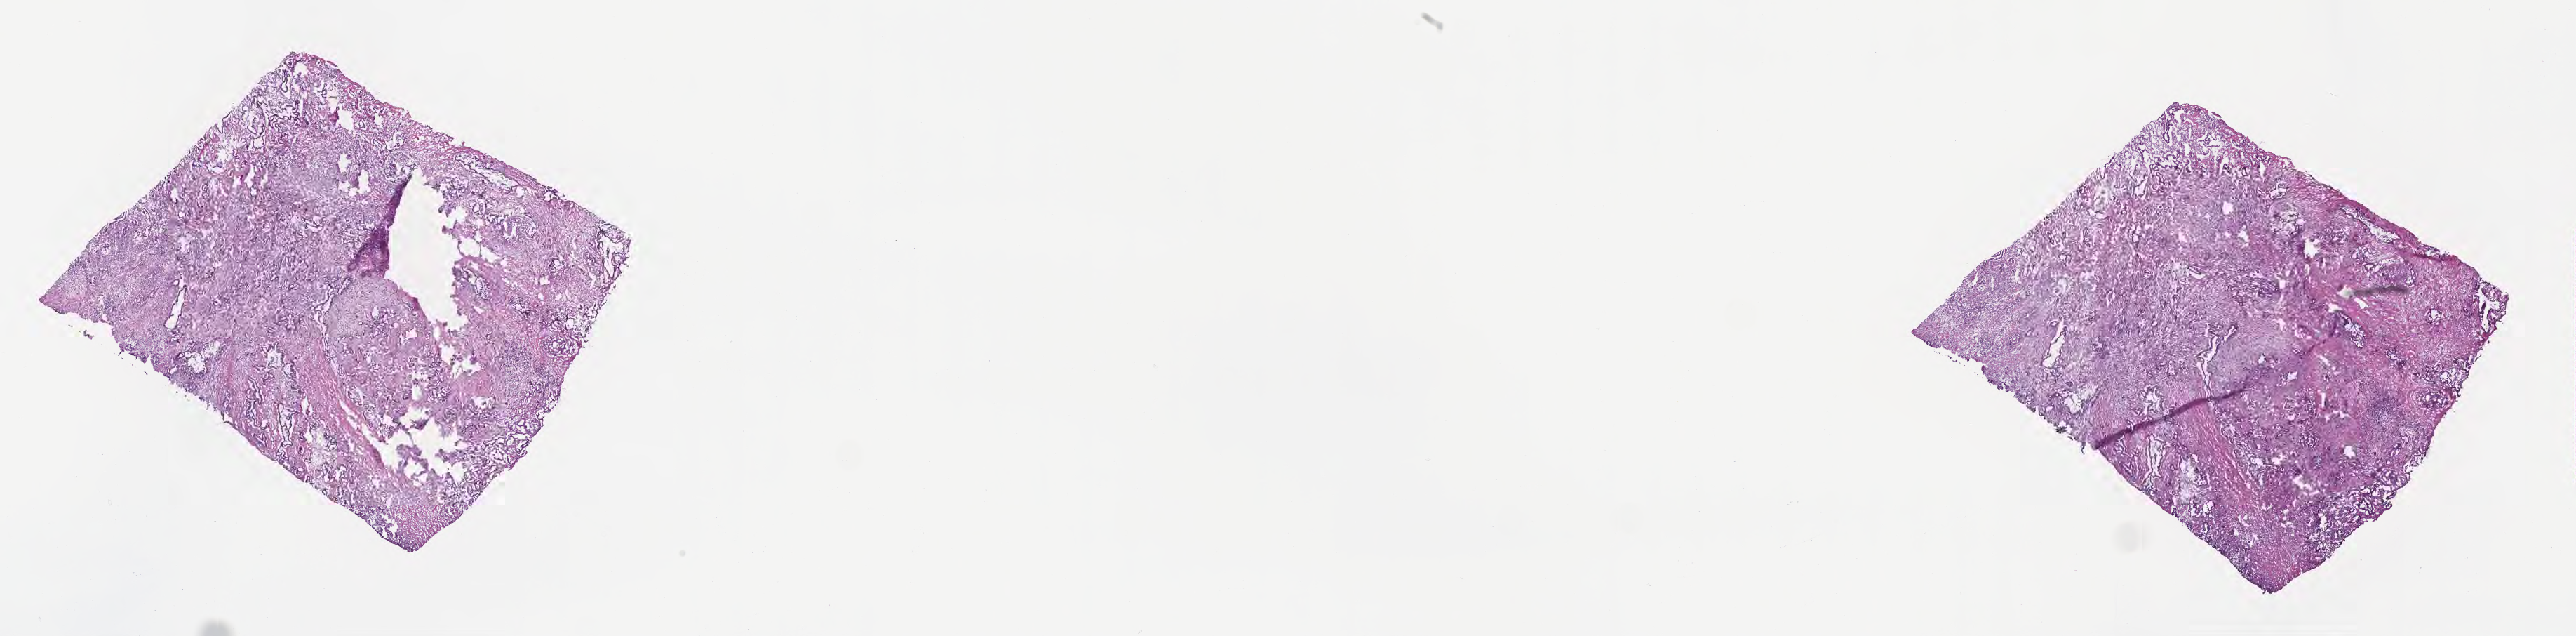
Digitized hematoxylin and eosin (H&E)-stained section — a low-resolution overview of the entire scanned area, about 29.7 x 7.3 mm; frozen section (tissue freezing medium); specimen: primary tumor; anatomic site: tail of pancreas. Male patient; age at initial diagnosis 72 years.
Diagnosis: Infiltrating duct carcinoma, NOS.